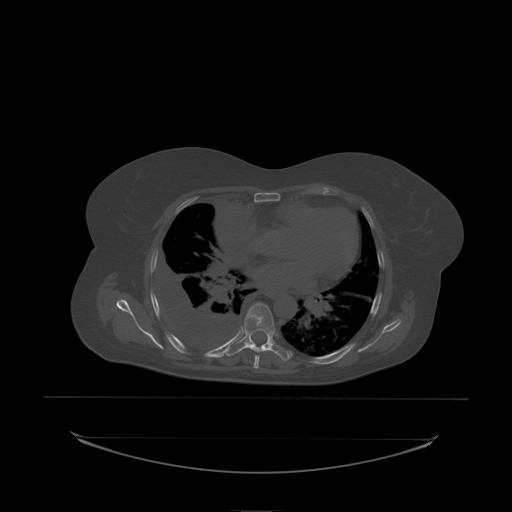
CT including the spine, one axial slice; position 144 of 242 along the scan axis; bone window (W 1800 / L 400 HU); 512 × 512 image matrix, field of view 500 × 500 mm. Female patient, age 53 years. Case-level facts recorded for this patient, not image findings: primary cancer: lung.
Annotated regions visible in this slice (semi-automatically segmented with operator editing):
- T7 vertebra: bounding box (x1, y1, x2, y2) in pixels: (244, 303, 275, 338)